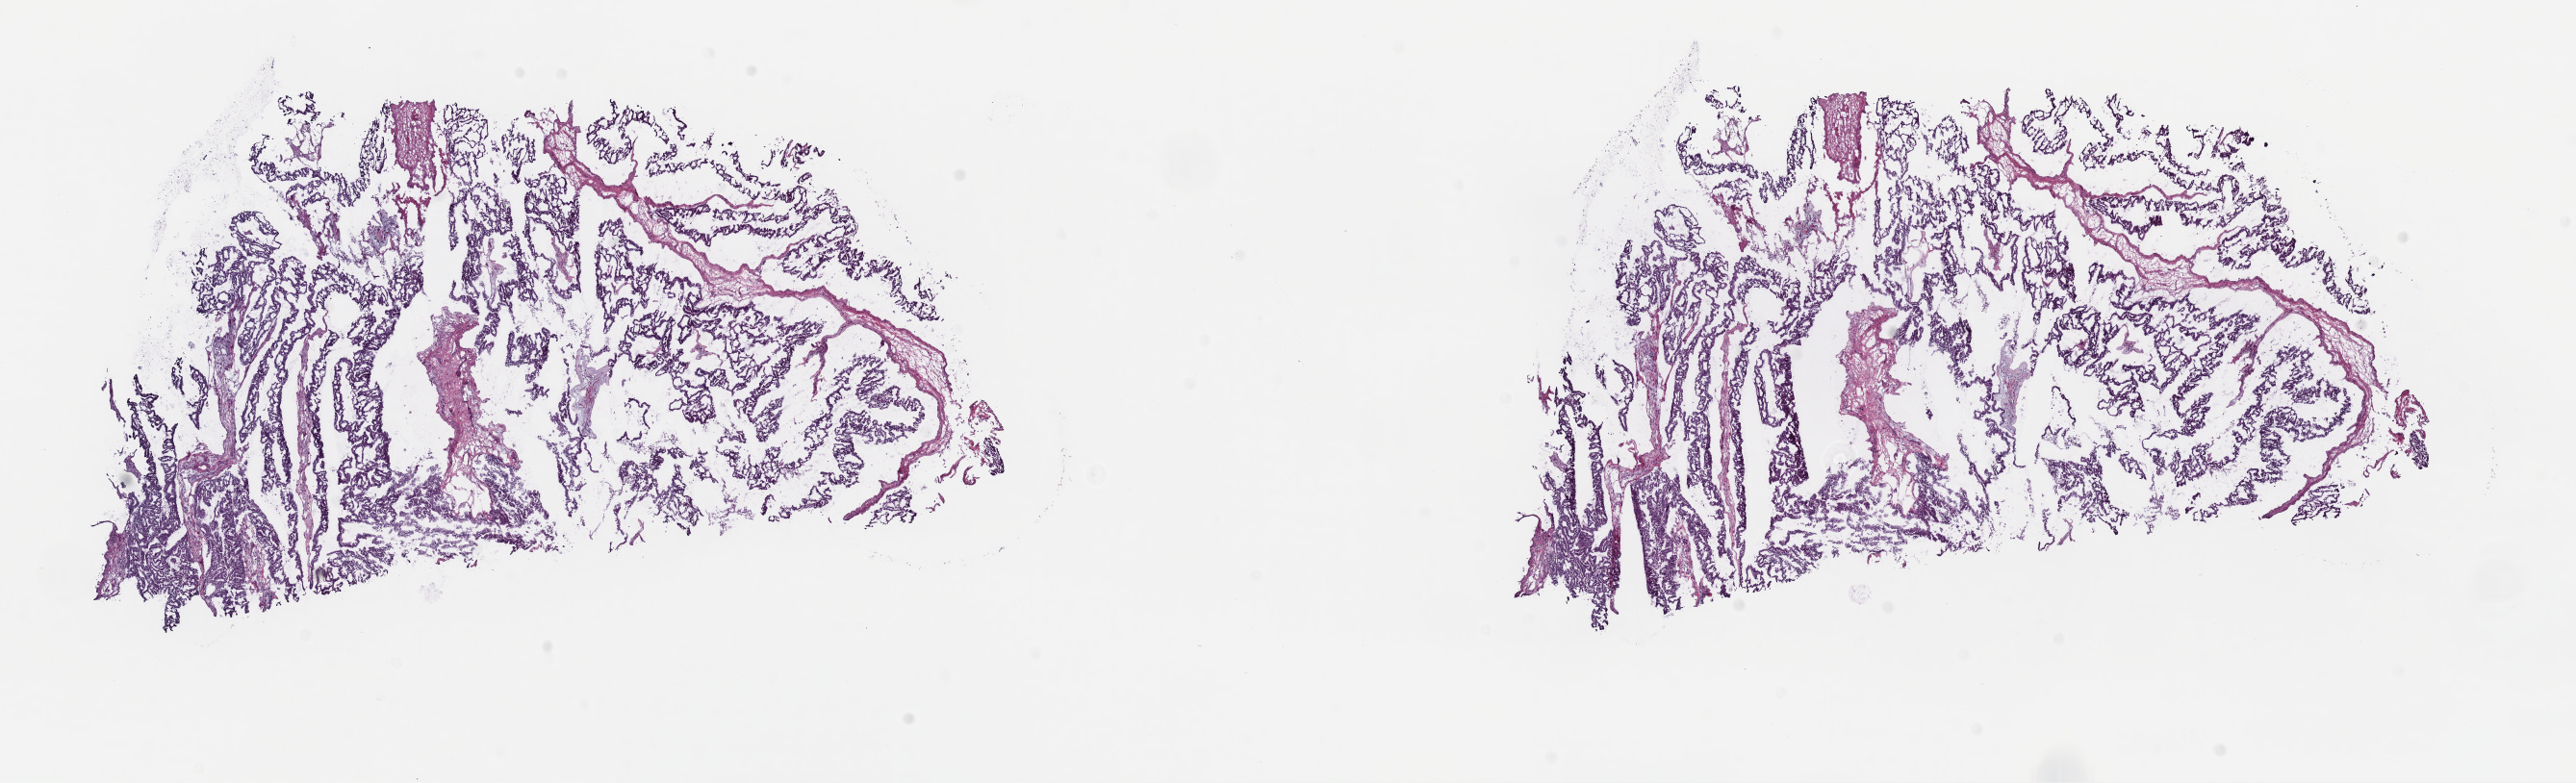
Whole-slide histology image, Hematoxylin and eosin (H&E) stained — whole scanned area (about 21.1 x 6.4 mm, slide scanned at 40x) shown as a low-resolution overview; frozen section; sample: primary tumour, cervix. Patient: female, age at initial diagnosis 48 years. Histologic grade: G2 (moderately differentiated). Composition of this section per pathologist review: tumour cells 100%, tumour nuclei 95%, normal cells 0%, stromal cells 0%, necrosis 0%. Infiltration values recorded for this section: lymphocyte infiltration 1%, monocyte infiltration 0%, neutrophil infiltration 0%.
Pathologic diagnosis: Adenocarcinoma, endocervical type (cervix uteri). FIGO stage: IVB. Lymph nodes positive (case pathology): 1 of 25 examined.